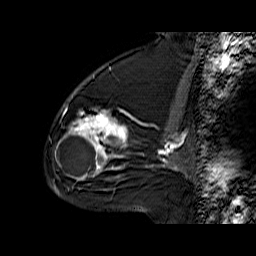
Breast MRI (dynamic contrast-enhanced), one sagittal slice. Slice 37 of 60 in the series (ordered by position). Dynamic contrast-enhanced series, time point 2 of 6 at this slice position (early post-contrast). 1.5 T. TE 6.3 ms, TR 32.9 ms. 4 mm slice thickness. 256 × 256 image matrix, field of view 200 × 200 mm. Female patient. Case-level facts recorded for this patient, not image findings: setting: breast cancer imaged before/during neoadjuvant chemotherapy; receptor status: triple-negative.
Outlined on this slice (semi-automatic segmentation, software-assisted and operator-edited):
- analysis volume of interest (the breast-tissue region the enhancement analysis was run in; not a lesion): bounding box <56,76,132,170> (left, top, right, bottom; pixels)
- tumour enhancement mask (voxels above the 100 % enhancement threshold inside the analysis volume of interest): <64,110,128,170>